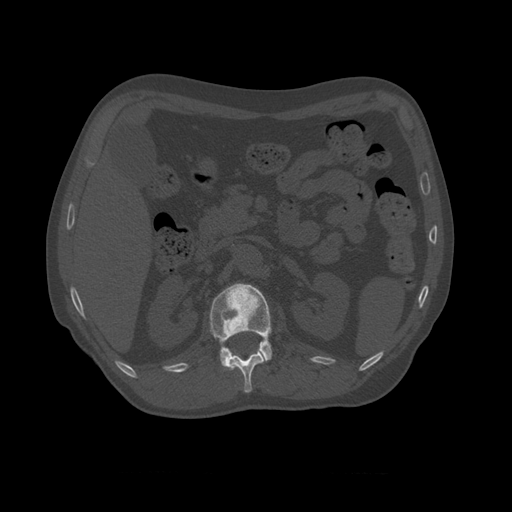
CT including the spine, one axial slice; position 365 of 450 along the scan axis; reconstruction kernel STANDARD; bone window (W 1800 / L 400 HU); 1.25 mm slice thickness; 512 × 512 image matrix, field of view 405 × 405 mm. Patient age 75 years. From the clinical record (not read from this slice): primary cancer: prostate.
Structures marked on this image (semi-automatic segmentation, software-assisted and operator-edited):
- L1 vertebra: bounding box (x1, y1, x2, y2) in pixels: (209, 283, 272, 371)
- T10 vertebra: (224, 345, 273, 366)
- T11 vertebra: (225, 350, 264, 393)